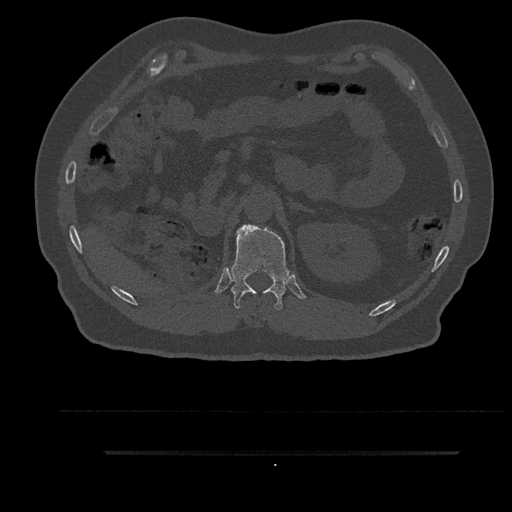
CT including the spine, one axial slice; slice 246 of 797 in the series (ordered by position); bone window (W 1800 / L 400 HU); 0.5 mm slice thickness; 512 × 512 image matrix. Patient: male, 63 years. From the clinical record (not read from this slice): primary cancer: renal; vertebrae with lytic lesions (as recorded): T8.
Outlined on this slice (semi-automatic segmentation, software-assisted and operator-edited):
- T12 vertebra: bounding box (x1, y1, x2, y2) in pixels: (229, 225, 291, 311)